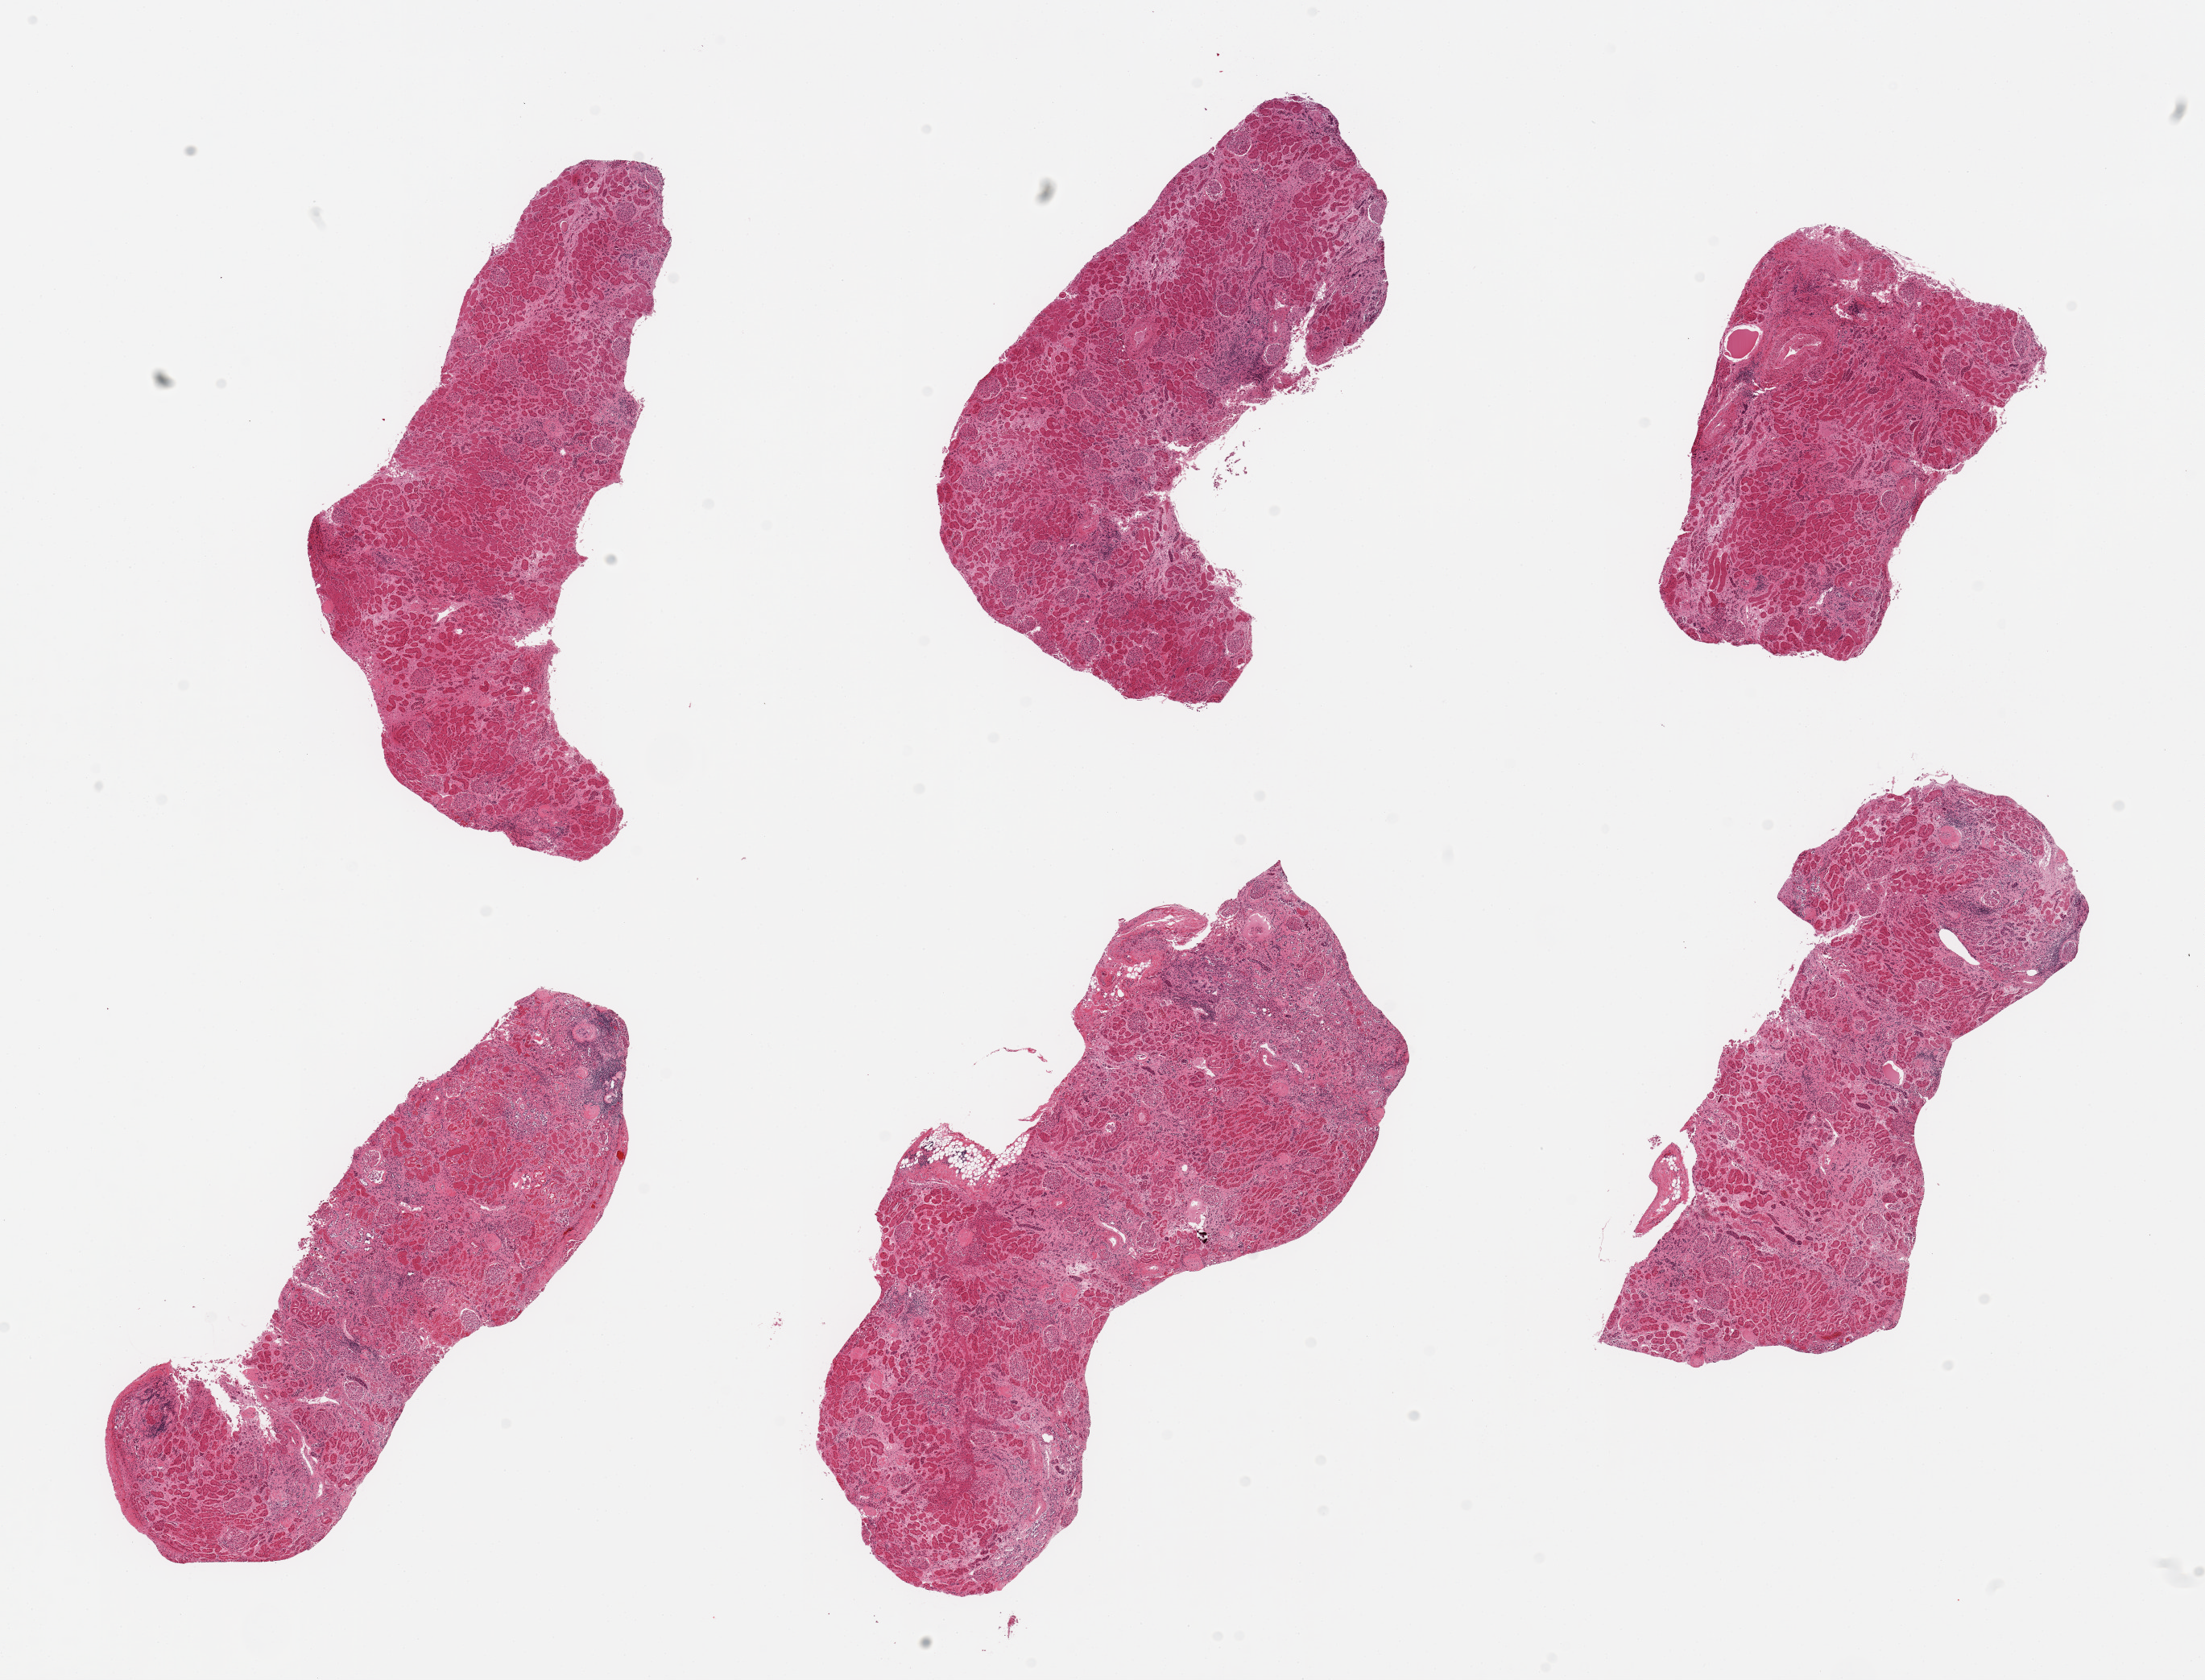
Whole-slide image, hematoxylin and eosin (H&E) stain, a low-resolution overview of the entire scanned area, about 21.7 x 16.5 mm (slide scanned at 20x). PAXgene-fixed paraffin-embedded (PFPE) section. Section of renal cortex (target tissue). Tissue donor sample. Donor sex: female.
Reviewer comment on this tissue sample: 6 pieces, glomeruli present, marked tubular autolysis.